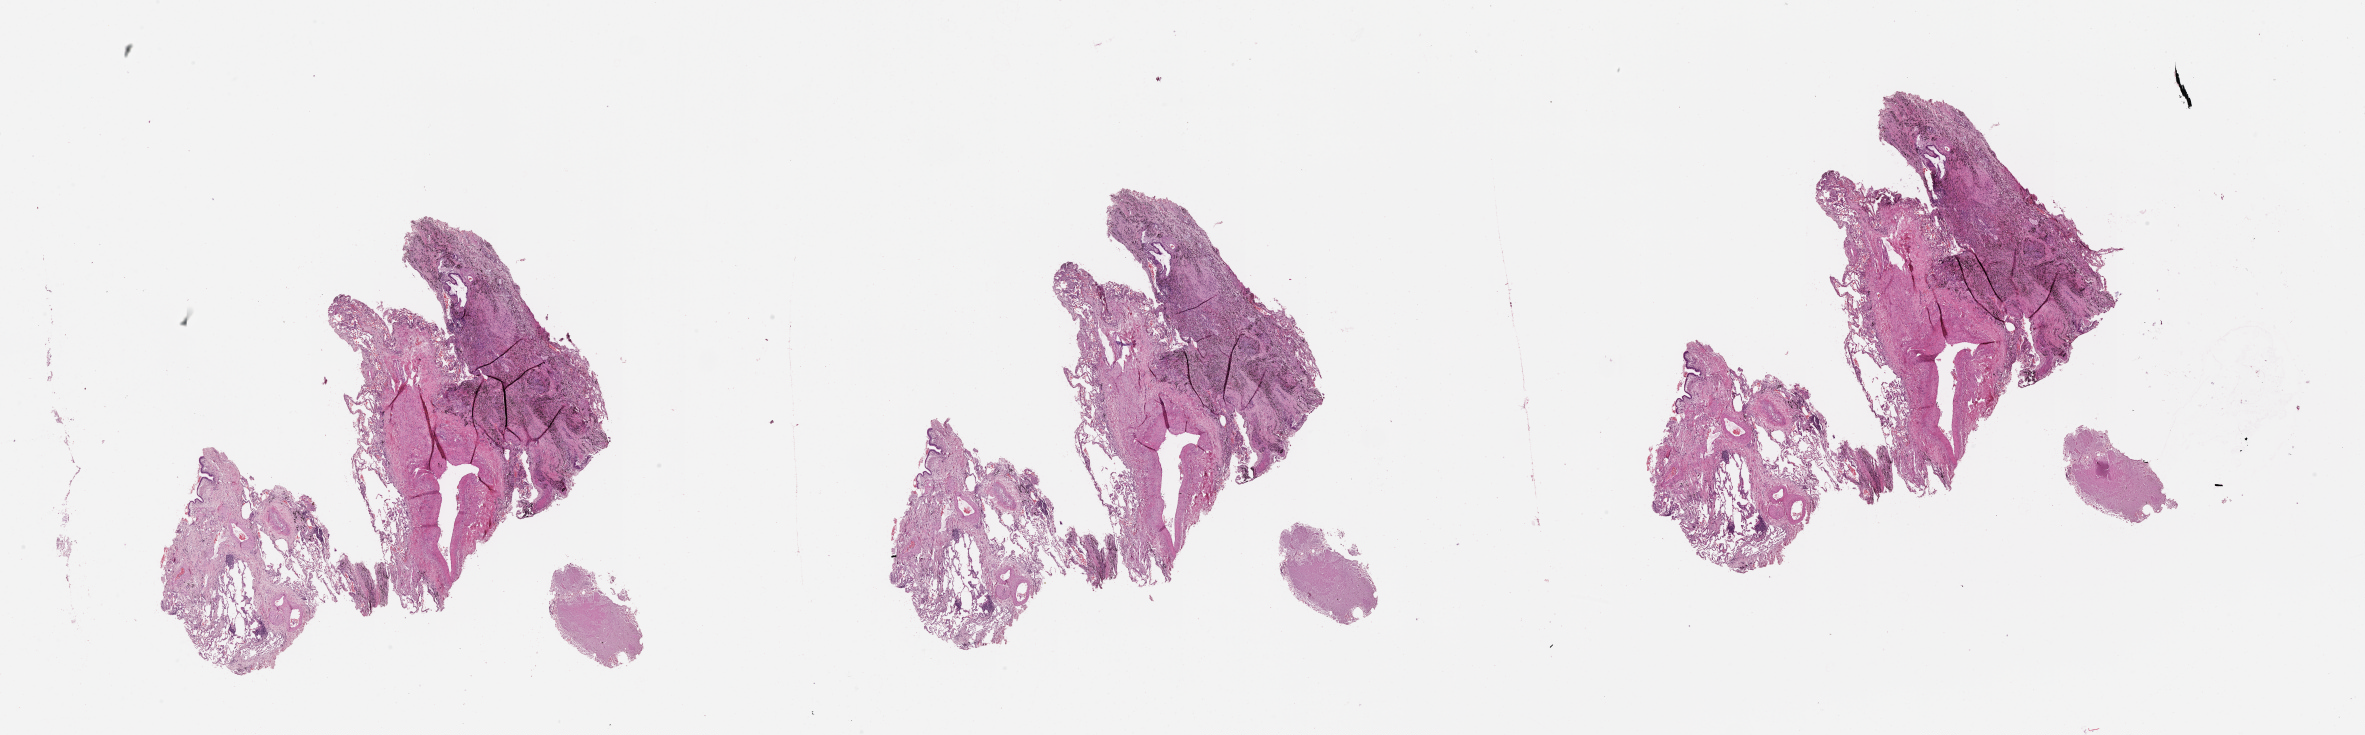
Digitized H&E-stained tissue section (whole slide) — whole scanned area (about 38.1 x 11.8 mm, acquisition: 20x scan) shown as a low-resolution overview; normal (non-tumour) tissue sample, lung. 68-year-old male patient.
* this section: normal (non-tumour) tissue from the same patient
* patient diagnosis (cohort enrolment): squamous cell carcinoma (lung)